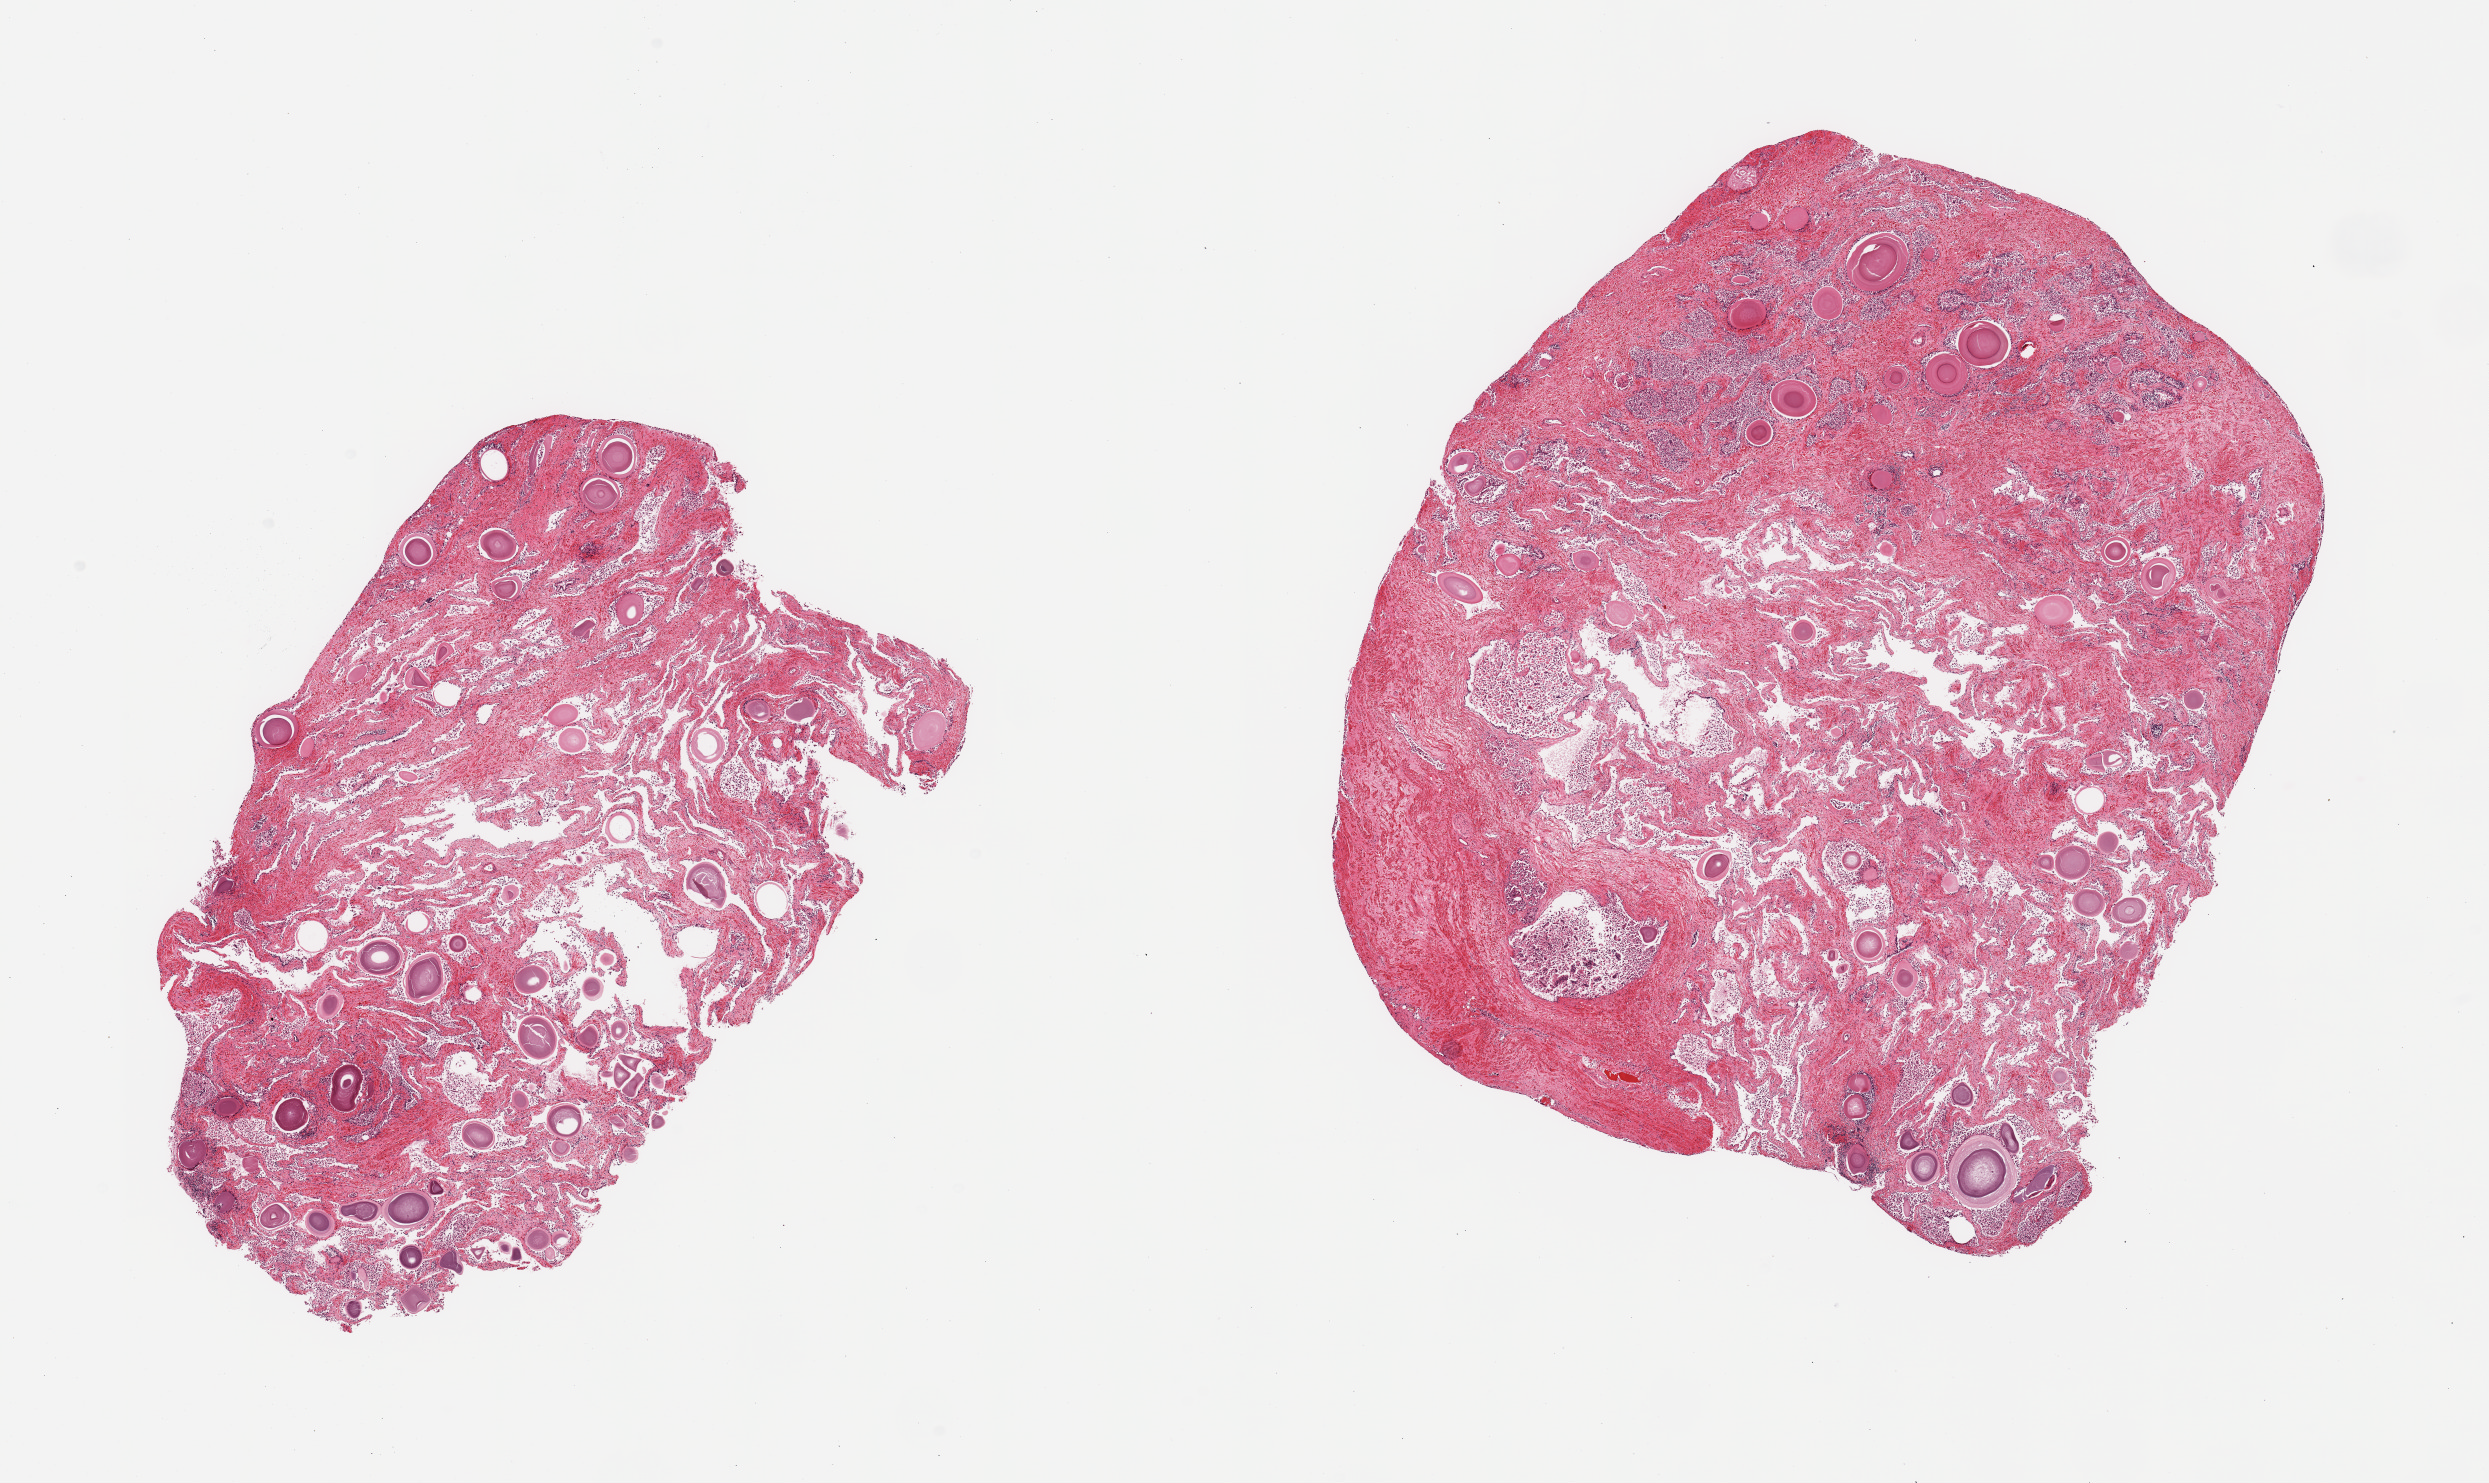
Digitized H&E-stained section, a low-resolution overview of the entire scanned area, about 19.7 x 11.7 mm (acquisition: 20x scan); PAXgene-fixed, paraffin-embedded tissue; sampled site (target tissue): prostate; tissue donor sample. Male donor.
Pathologist's review note for this sample: 2 pieces; moderate to severe glandular autolysis with abundance of coropora amylacea.